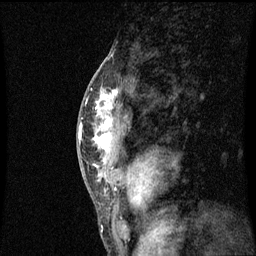
Breast MRI (dynamic contrast-enhanced), one sagittal slice; position 38 of 60 along the scan axis; dynamic contrast-enhanced series, image 2 of 3 at this slice position (ordered by acquisition); 1.5 T; TE 4.2 ms, TR 8.9 ms; 2 mm slice thickness; 256 × 256 image matrix, field of view 200 × 200 mm. Female patient, age 50 years. From the clinical record (not read from this slice): setting: breast cancer imaged before/during neoadjuvant chemotherapy; receptor status: triple-negative.
Structures marked on this image (semi-automatic segmentation, software-assisted and operator-edited):
- analysis volume of interest (the breast-tissue region the enhancement analysis was run in; not a lesion): box from (x=84, y=80) to (x=129, y=171) px
- tumour enhancement mask (voxels above the 70 % enhancement threshold inside the analysis volume of interest): (x=94, y=90)–(x=119, y=167)